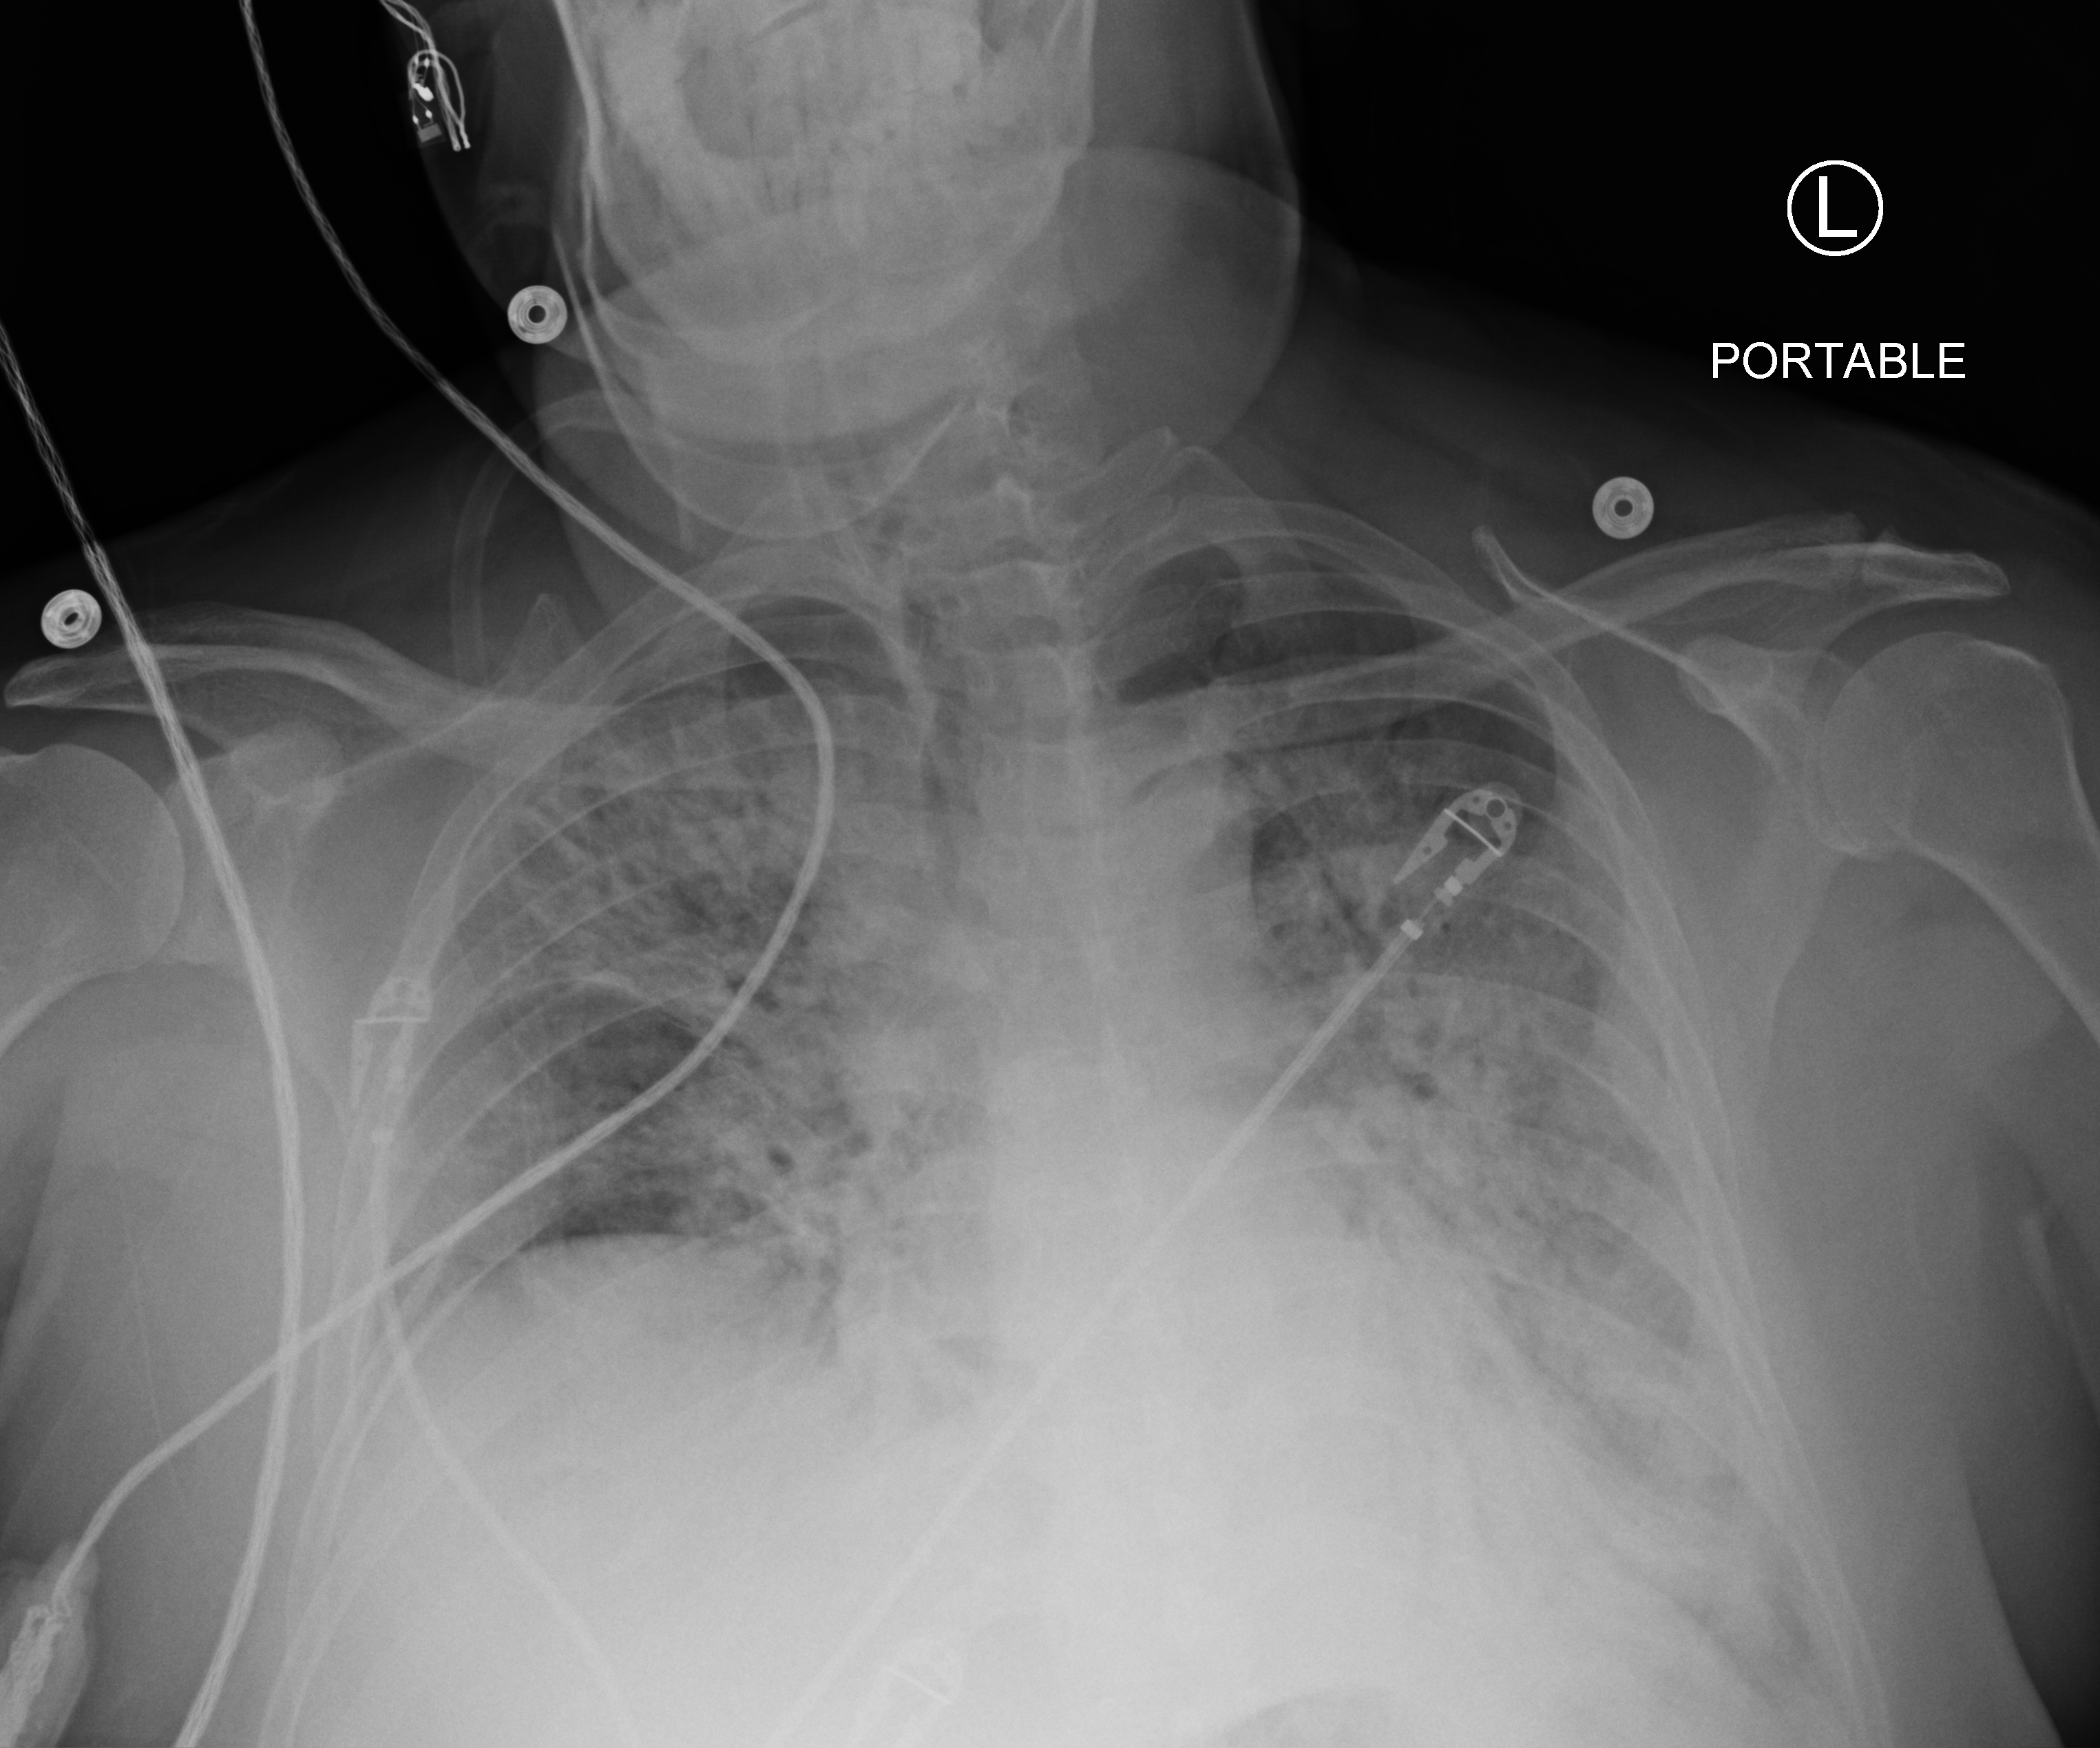
Portable chest radiograph. Patient hospitalised with COVID-19; male, aged 18–59 years.
Admission-level facts for this patient (not findings on this image; timing relative to this image not recorded): length of hospital stay: 35 days; admitted to intensive care during this hospital stay: yes; mechanically ventilated during this hospital stay: yes.